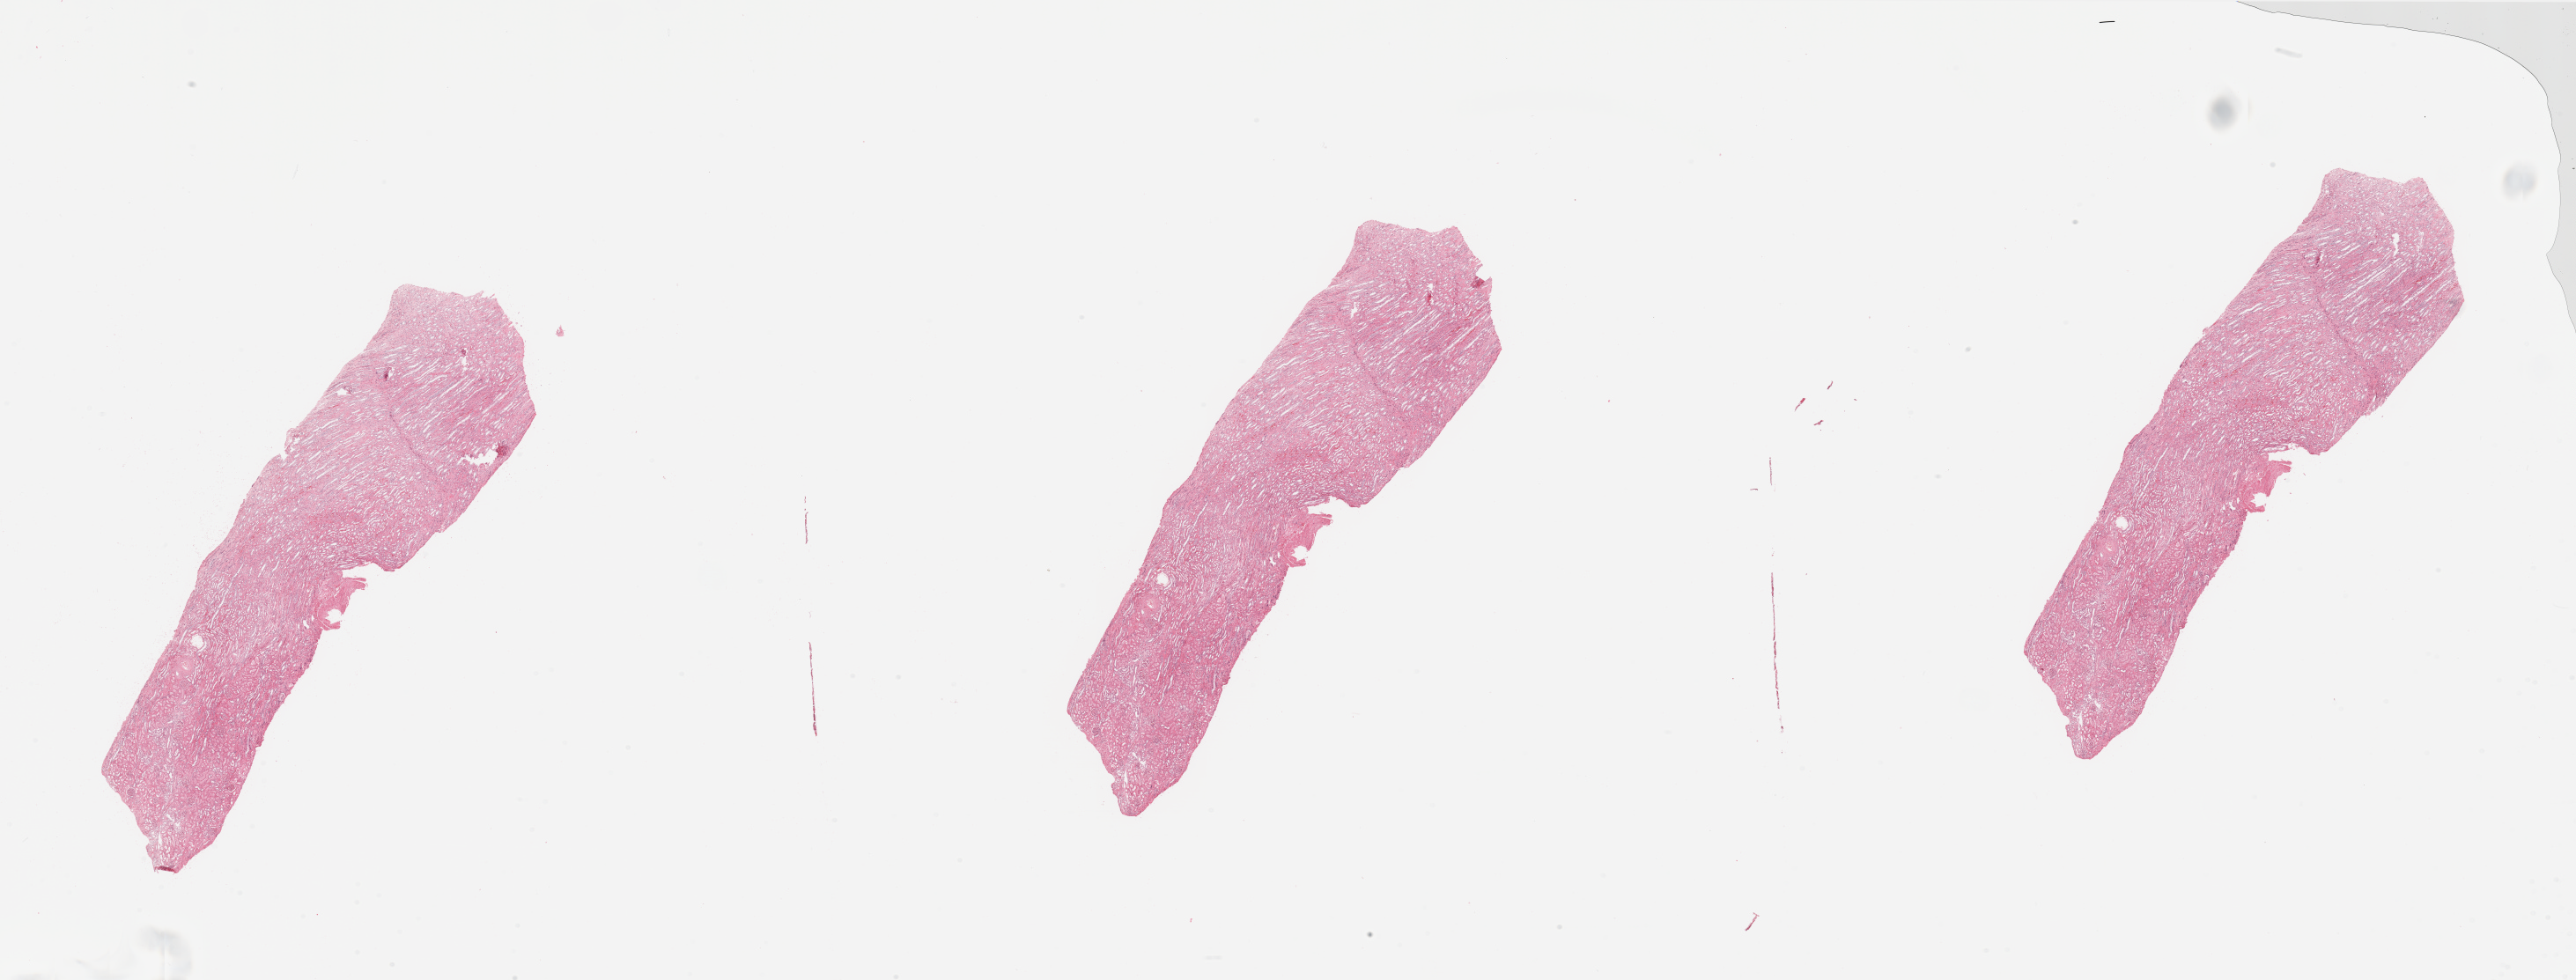
Whole-slide histology image, Hematoxylin and eosin (H&E) stained — shown as a low-resolution overview of the whole scanned area (about 46.3 x 17.6 mm, from a 20x scan). Normal (non-tumour) tissue sample, sampled site: kidney. Male, 56 y/o.
This section: normal (non-tumour) tissue from the same patient. Patient diagnosis: Renal cell carcinoma, NOS.